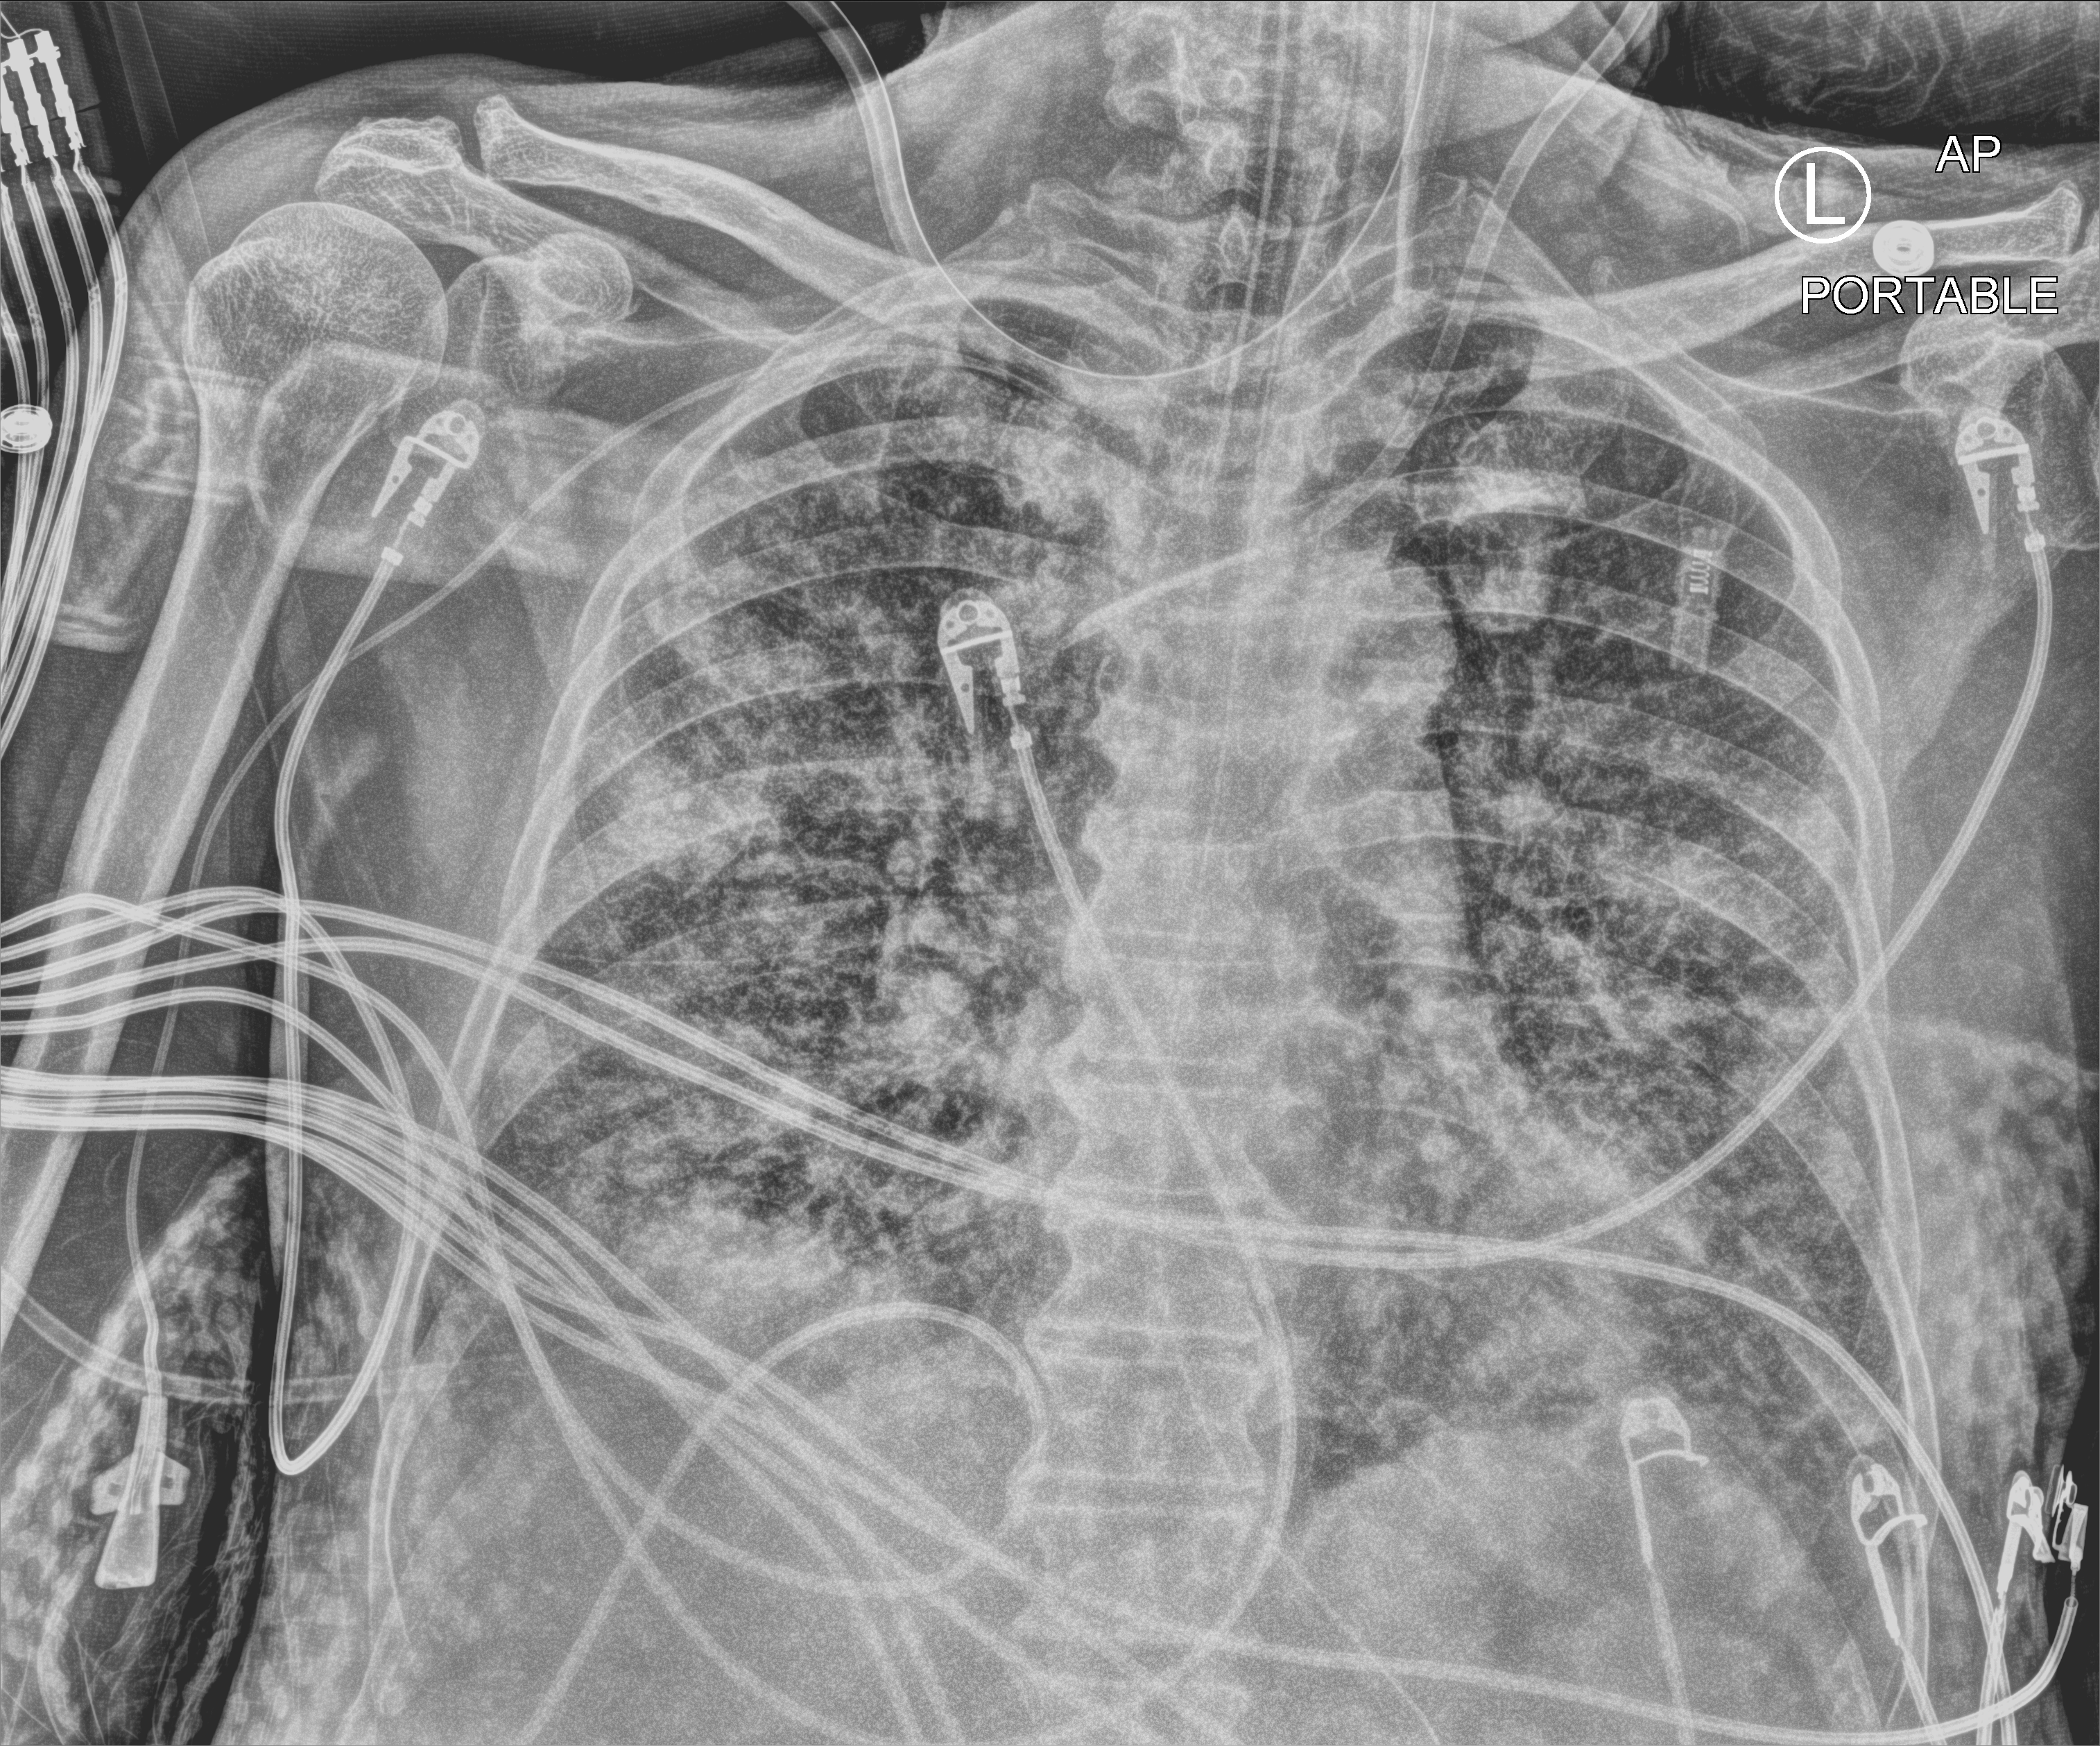
Chest X-ray (portable); anteroposterior (AP) projection. Male patient hospitalised with COVID-19, age 60–74 years.
Admission-level facts for this patient (not findings on this image; timing relative to this image not recorded):
- mechanically ventilated during this hospital stay: yes